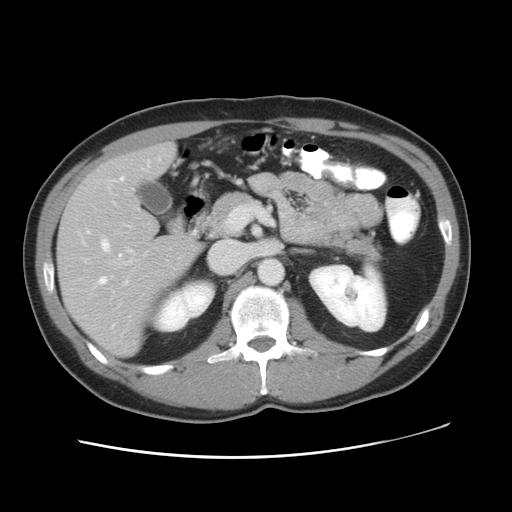
Contrast-enhanced abdominal CT, one axial slice; position 26 of 49 along the scan axis; reconstruction kernel STANDARD; 120 kVp; intravenous contrast given; soft-tissue window (W 400 / L 40 HU); 5 mm slice thickness; 512 × 512 image matrix, field of view 363 × 363 mm. Male patient, age 41 years. From the clinical record (not read from this slice): diagnosis: colorectal cancer liver metastases, imaged before liver resection; multiple liver metastases: yes; largest metastasis: 0.7 cm; disease in both lobes: yes.
Outlined on this slice (outlined manually by an expert reader):
- hepatic veins: box from (x=96, y=157) to (x=238, y=286) px
- liver: (x=58, y=145)–(x=198, y=355)
- planned liver remnant (the part of the liver to remain after resection): (x=109, y=145)–(x=175, y=189)
- portal vein (with intrahepatic branches): (x=125, y=281)–(x=128, y=283)